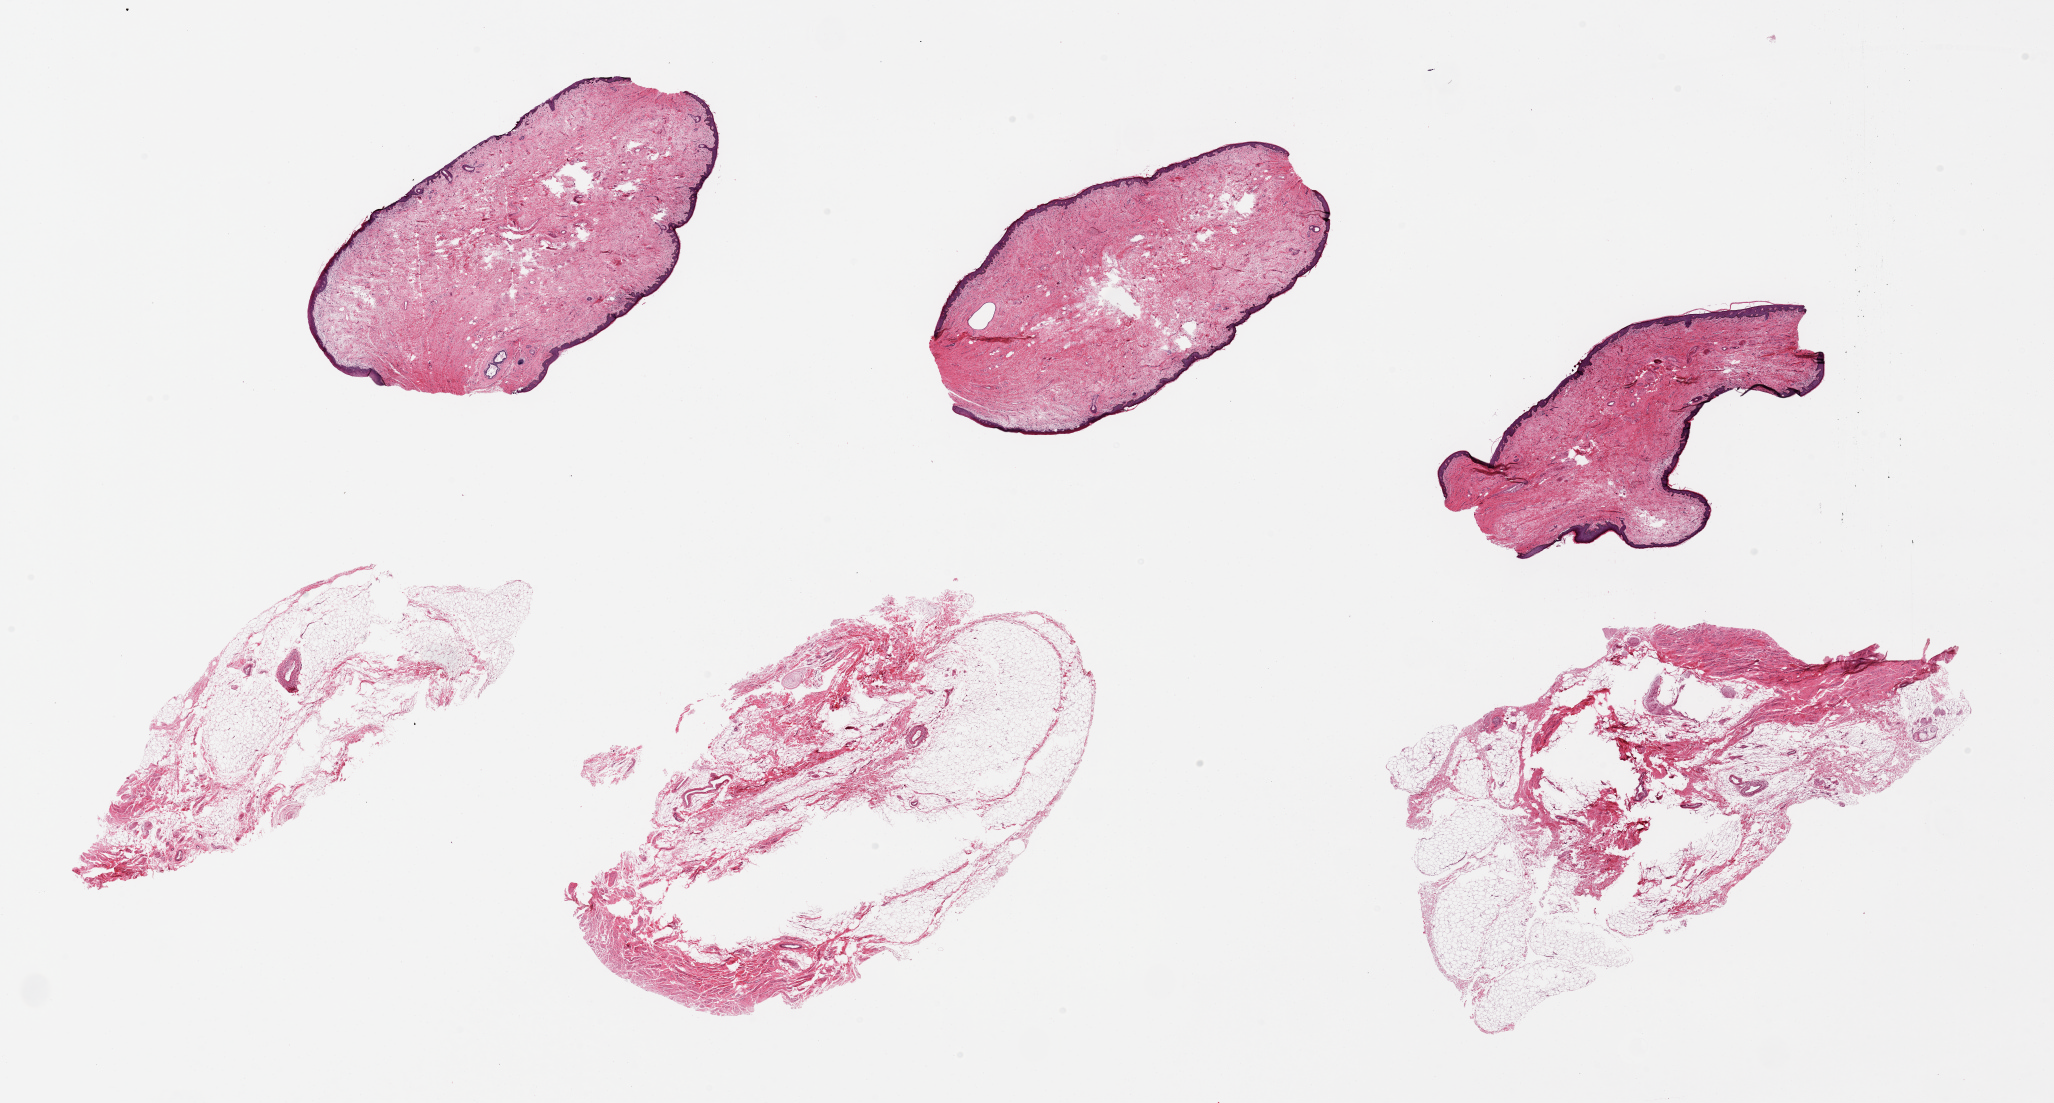
Digitized hematoxylin and eosin (H&E)-stained section, brightfield, low-resolution overview of the scanned area, about 32.5 x 17.4 mm (from a 20x scan); PAXgene-fixed, paraffin-embedded tissue; sampled site (target tissue): vagina; tissue donor sample. Donor: female.
Review note (as recorded): 6 pieces, up to 10x5mm; 3 show squamous mucosa up to ~100 microns, 3 are all stroma.